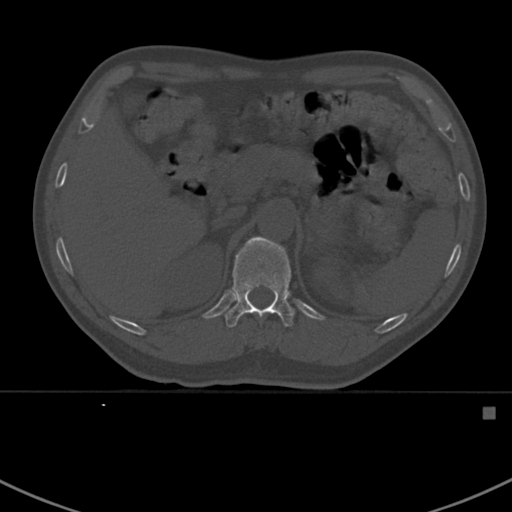
CT including the spine, one axial slice. Position 331 of 412 along the scan axis. 120 kVp. Bone window (W 1800 / L 400 HU). 512 × 512 image matrix, field of view 358 × 358 mm. Male patient, age 59 years. From the clinical record (not read from this slice): primary cancer: prostate.
Annotated regions visible in this slice (semi-automatically segmented with operator editing):
- T12 vertebra: bounding box (x1, y1, x2, y2) in pixels: (225, 237, 295, 327)